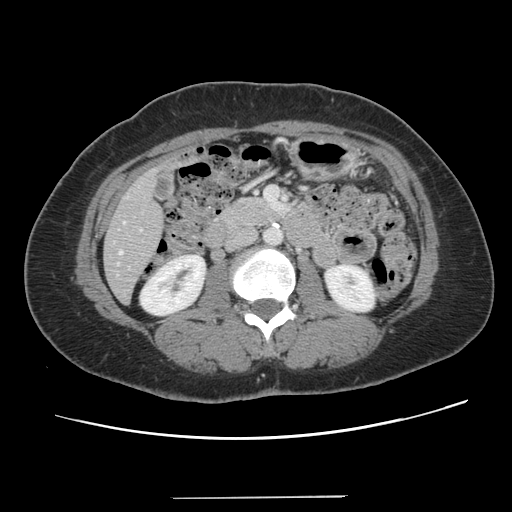
Contrast-enhanced abdominal CT, one axial slice. 120 kVp. Intravenous contrast given. Soft-tissue window (W 400 / L 40 HU). 2.5 mm slice thickness. 512 × 512 image matrix, field of view 366 × 366 mm. Female patient, age 53 years. Case-level facts recorded for this patient, not image findings: diagnosis: colorectal cancer liver metastases, imaged before liver resection; multiple liver metastases: no; largest metastasis: 14.5 cm; chemotherapy before resection: yes.
Outlined on this slice (expert manual segmentation):
- hepatic veins: bounding box (x1, y1, x2, y2) in pixels: (119, 251, 122, 254)
- liver: (105, 165, 164, 302)
- planned liver remnant (the part of the liver to remain after resection): (104, 216, 163, 302)